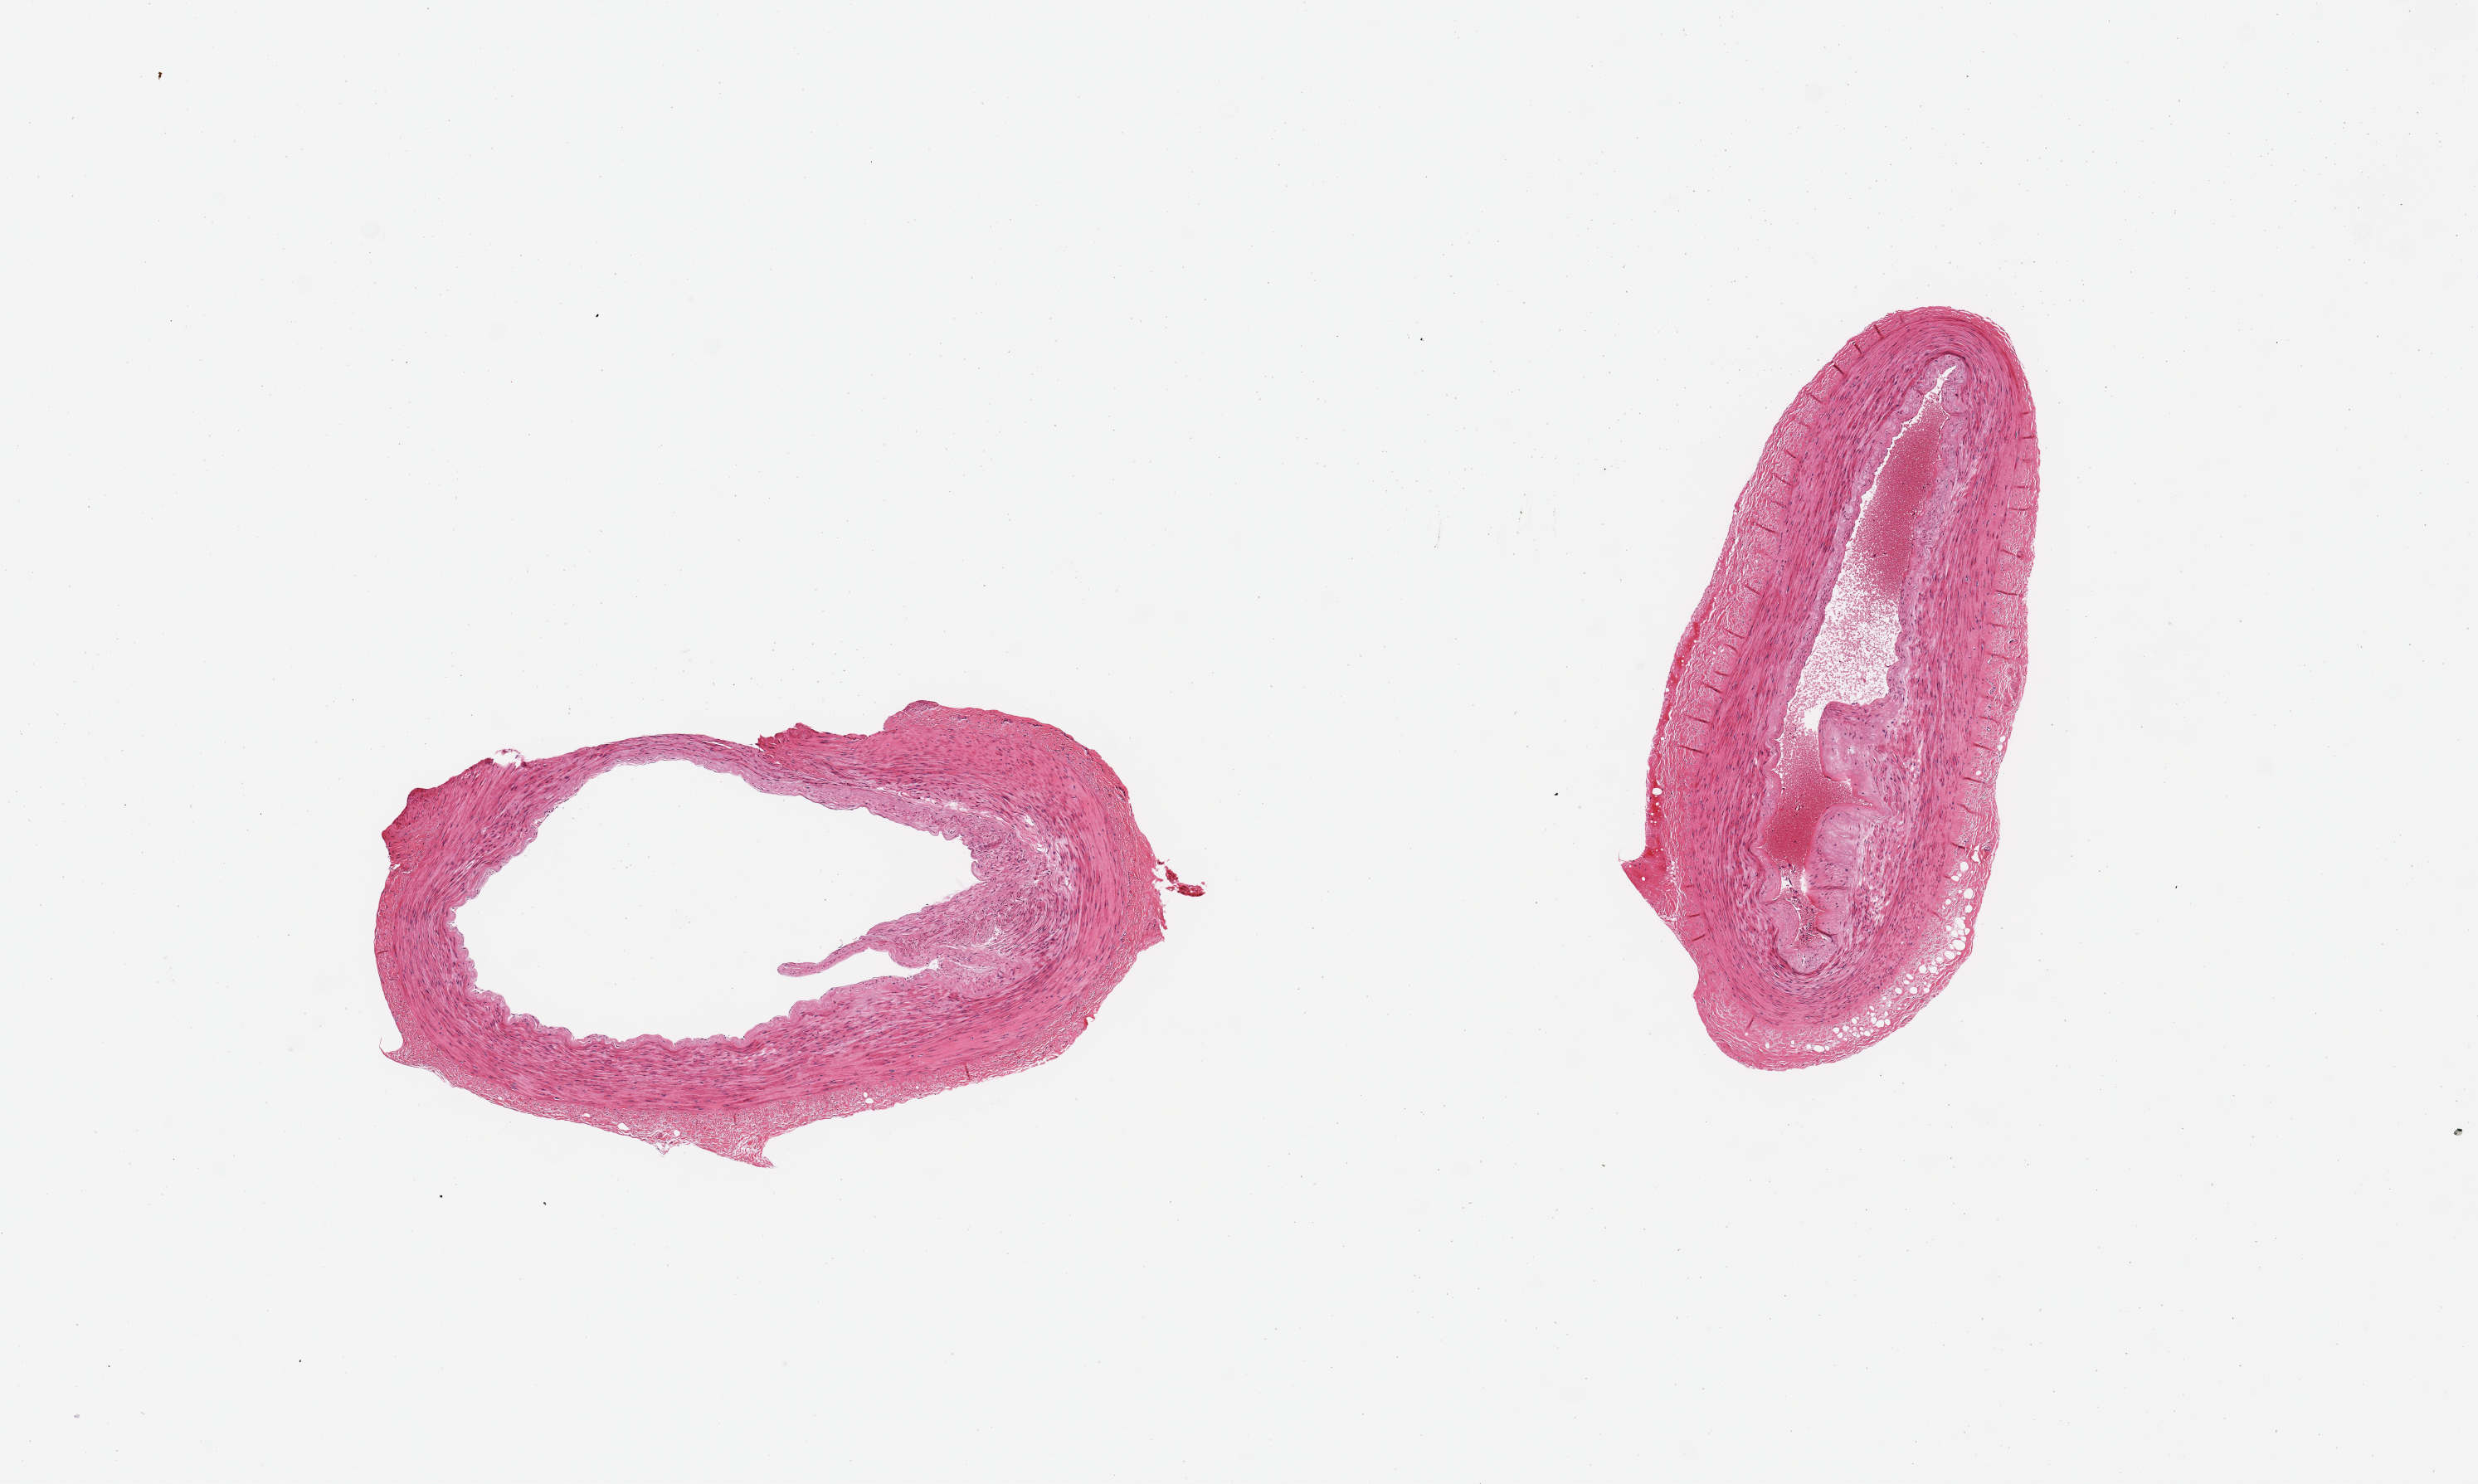
Haematoxylin and eosin whole-slide image, brightfield — a low-resolution overview of the entire scanned area, about 11.8 x 7.1 mm. PAXgene-fixed, paraffin-embedded tissue. Section of tibial artery (target tissue). Tissue donor sample.
Pathologist's review note for this sample: 2 pieces, no adherent fat; ~20% occlusive luminal atherosis.